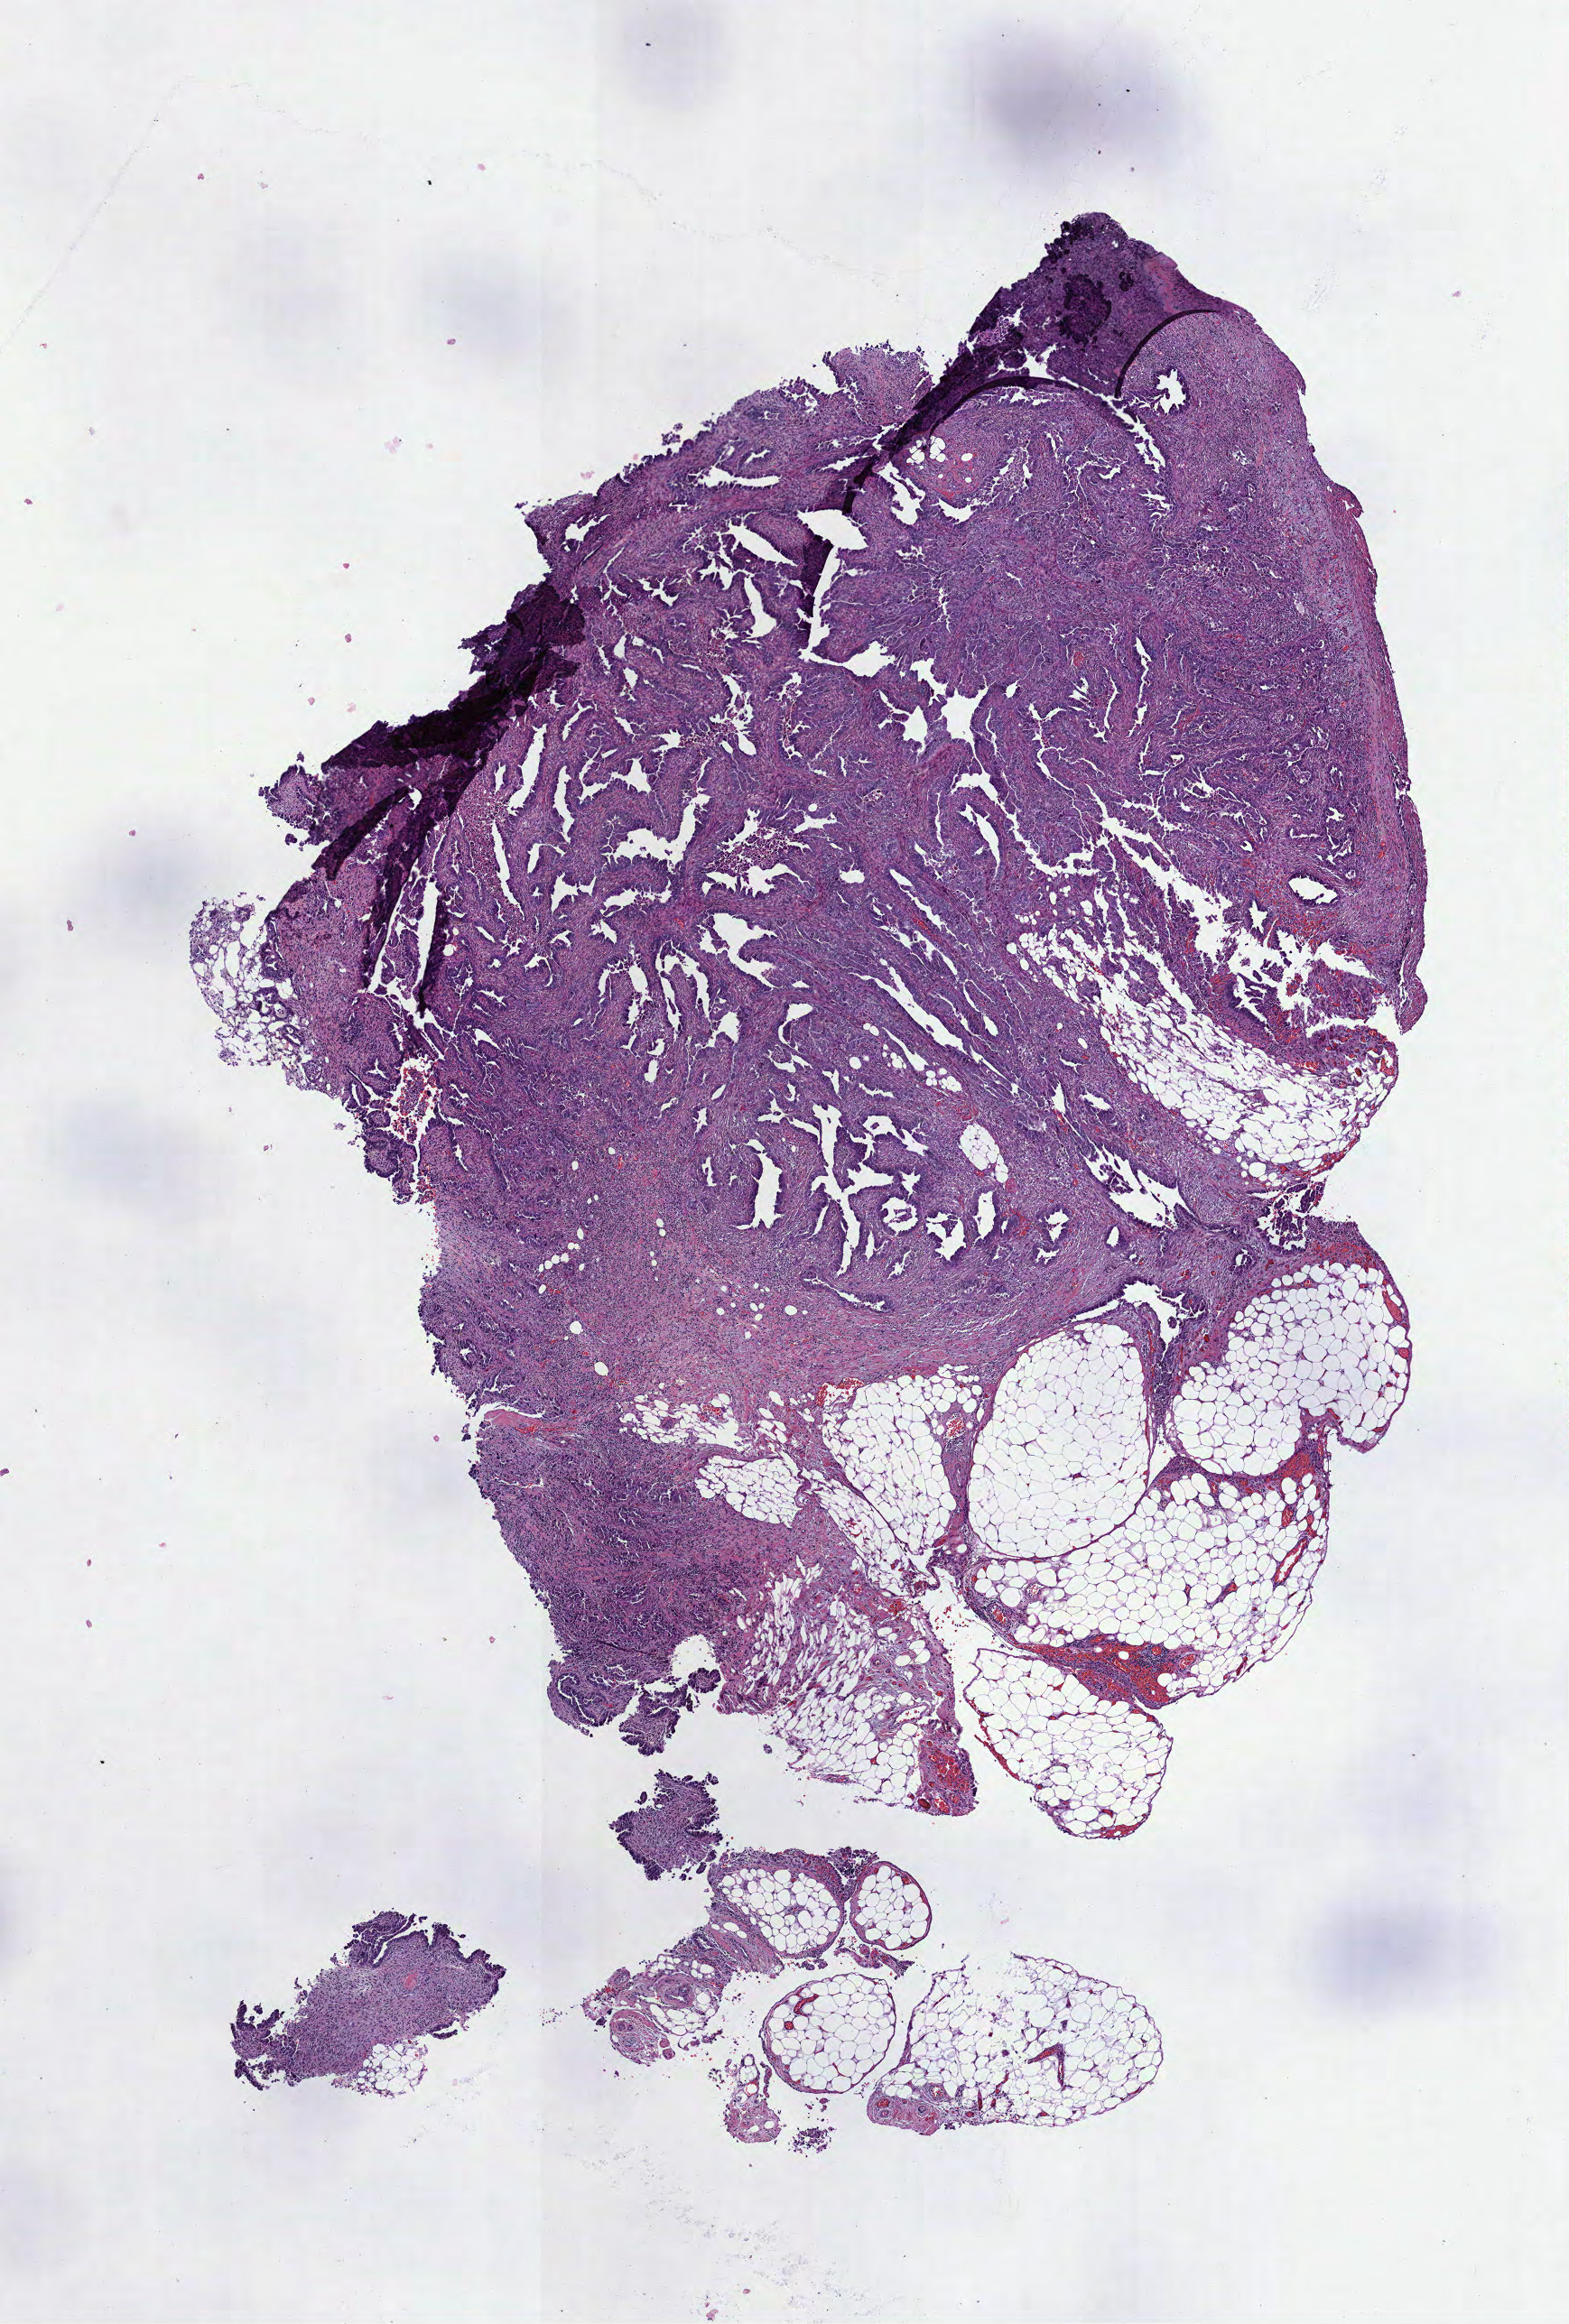
Hematoxylin and eosin (H&E) stained whole-slide image — whole scanned area (about 7.0 x 10.4 mm, from a 40x scan) shown as a low-resolution overview; FFPE section; primary tumour sample from the uterus. Female patient; age at initial diagnosis 70 years. Histologic grade: G3 (poorly differentiated).
- FIGO stage: IIIA
- histologic diagnosis: Serous cystadenocarcinoma, NOS (endometrium)